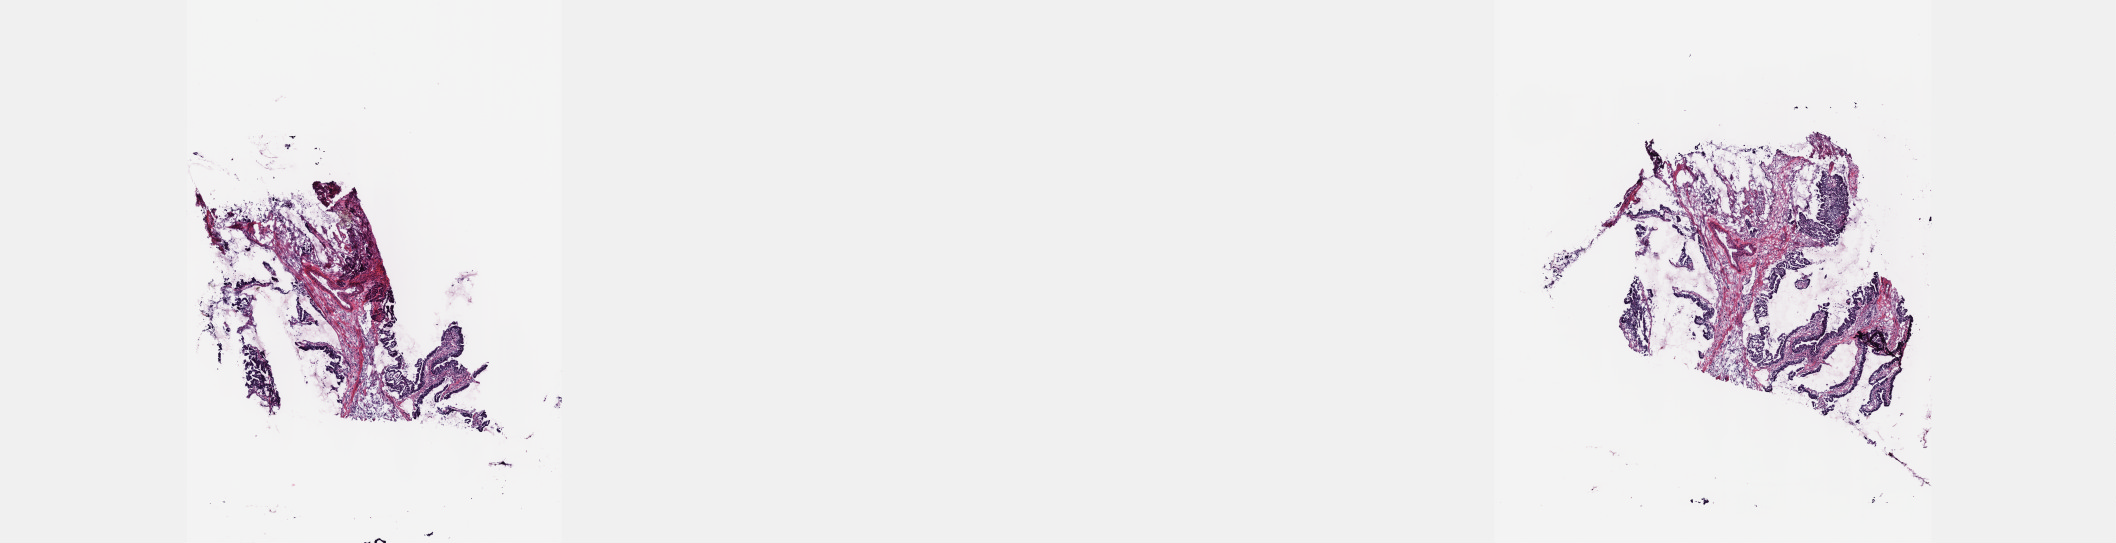
Whole-slide histology image, H&E-stained — a low-resolution overview of the entire scanned area, about 17.1 x 4.4 mm. Frozen section from the top of the tissue portion. Primary tumour sample from the cervix. Patient: female, age at initial diagnosis 34 years. Histologic grade: G2 (moderately differentiated). Slide review estimates, as recorded: tumour cells 60%, tumour nuclei 60%, normal cells 0%, stromal cells 30%, necrosis 10%. Infiltration values recorded for this section: lymphocyte infiltration 20%, monocyte infiltration 20%, neutrophil infiltration 40%.
FIGO stage: IB1. Lymph nodes positive (case pathology): 0 of 22 examined. Pathologic diagnosis: Mucinous adenocarcinoma (cervix uteri).